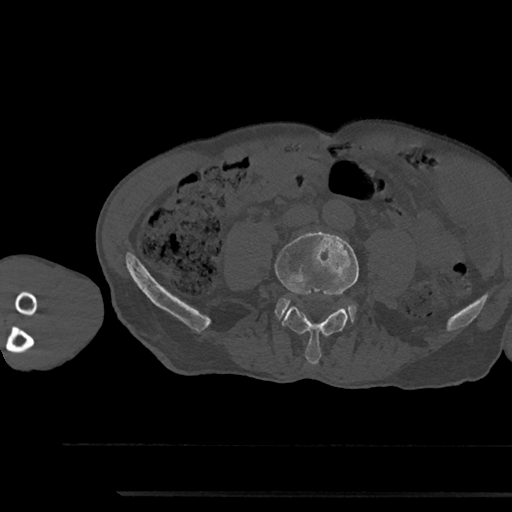
CT including the spine, one axial slice; position 394 of 797 along the scan axis; reconstruction kernel Br40s/3; bone window (W 1800 / L 400 HU); 0.5 mm slice thickness; 512 × 512 image matrix. Male patient, age 79 years. Case-level facts recorded for this patient, not image findings: primary cancer: prostate.
Annotated regions visible in this slice (semi-automatic segmentation, software-assisted and operator-edited):
- L4 vertebra: bounding box (x1, y1, x2, y2) in pixels: (275, 232, 359, 365)
- L5 vertebra: (277, 298, 355, 321)